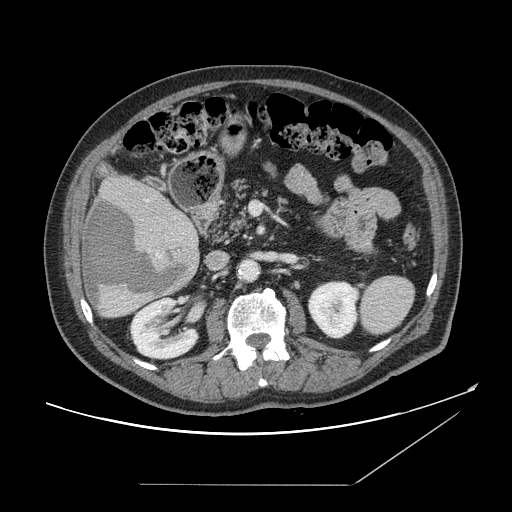
Contrast-enhanced abdominal CT, one axial slice; slice 71 of 166 in the series (ordered by position); 120 kVp; intravenous contrast given; soft-tissue window (W 400 / L 40 HU); 2.5 mm slice thickness; 512 × 512 image matrix, field of view 416 × 416 mm. Male patient, age 80 years. From the clinical record (not read from this slice): diagnosis: colorectal cancer liver metastases, imaged before liver resection; multiple liver metastases: no; largest metastasis: 2.2 cm.
Annotated regions visible in this slice (outlined manually by an expert reader):
- hepatic veins: box from (x=146, y=200) to (x=148, y=203) px
- liver: (x=81, y=174)–(x=200, y=318)
- planned liver remnant (the part of the liver to remain after resection): (x=106, y=173)–(x=184, y=218)
- liver metastasis: (x=85, y=199)–(x=193, y=308)